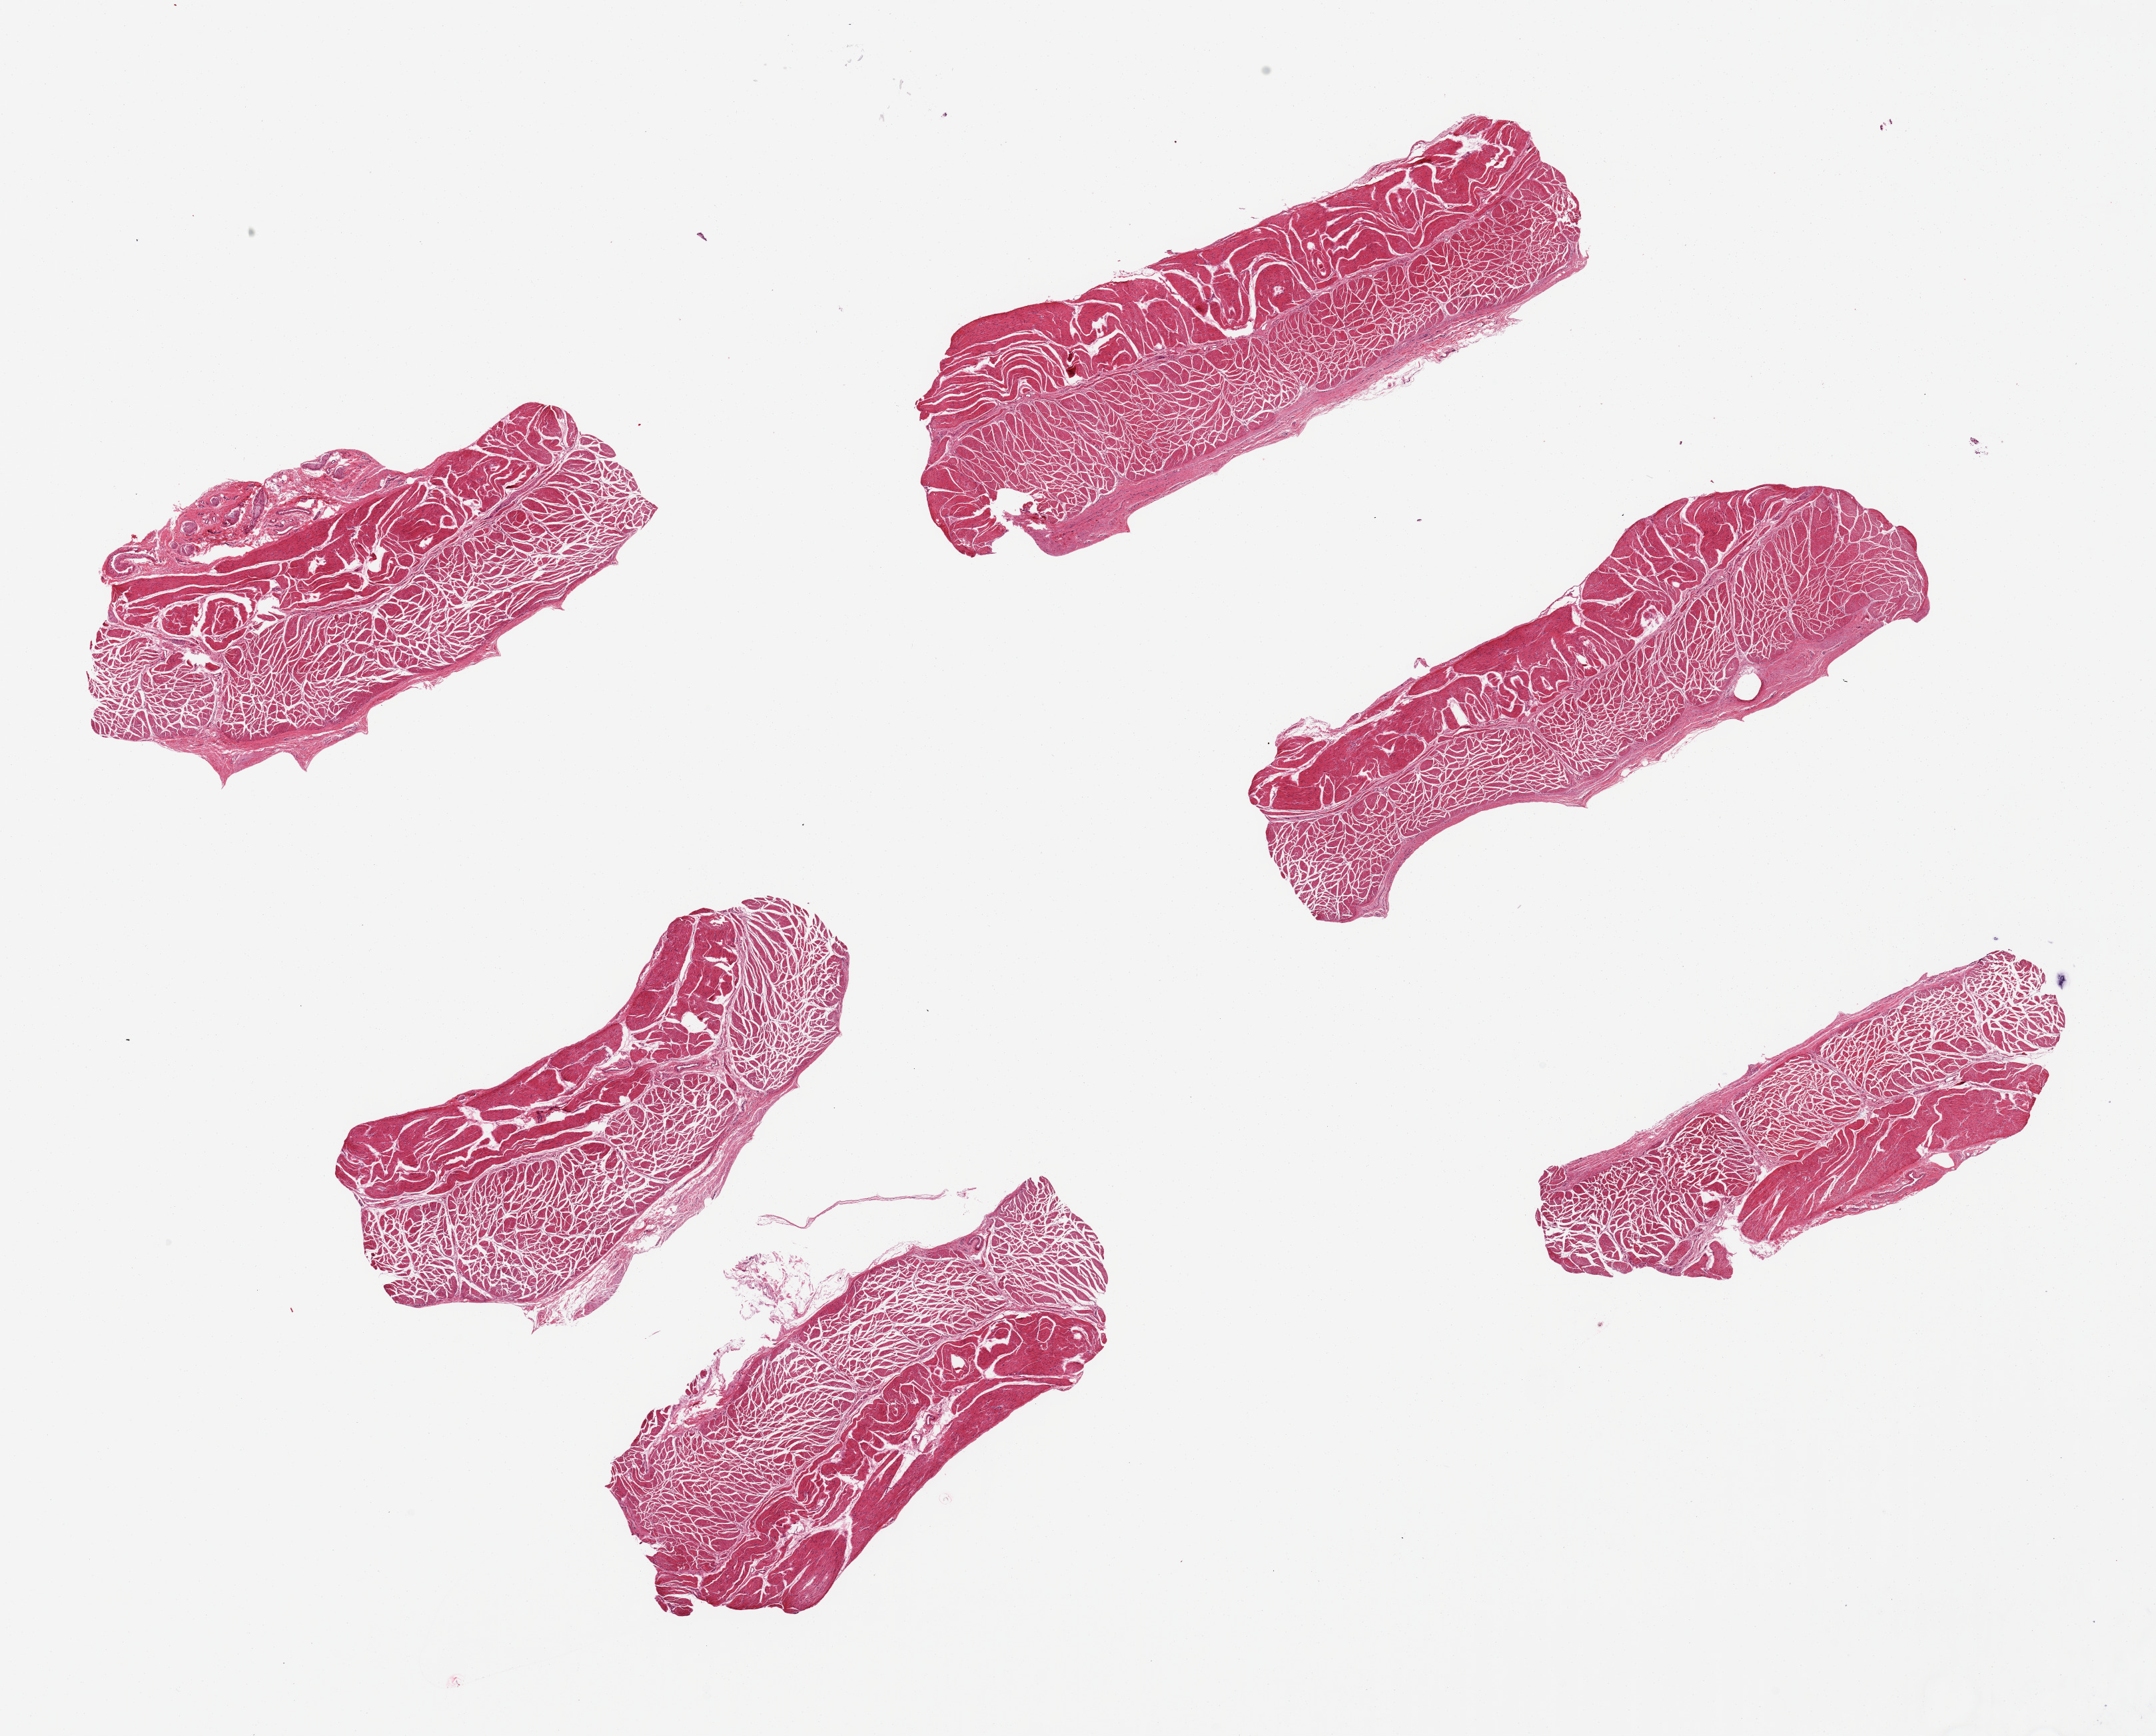
Digitized H&E-stained section, shown as a low-resolution overview of the whole scanned area (about 25.6 x 20.6 mm, slide scanned at 20x). PAXgene-fixed paraffin-embedded (PFPE) section. Sampled site (target tissue): esophageal muscle. Donor tissue sample. Female donor.
Review note (as recorded): 6 pieces, ~8.5x3 mm. well-oriented specimens.